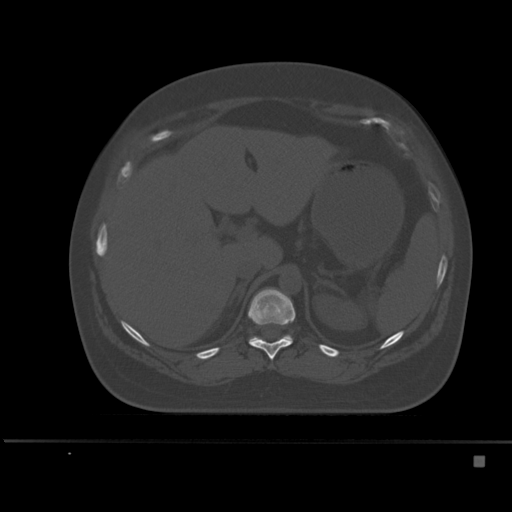
CT including the spine, one axial slice; position 227 of 495 along the scan axis; bone window (W 1800 / L 400 HU); 512 × 512 image matrix, field of view 404 × 404 mm. Patient: female, 33 years. Case-level facts recorded for this patient, not image findings: primary cancer: breast; vertebrae with lytic lesions (as recorded): T1.
Annotated regions visible in this slice (semi-automatically segmented with operator editing):
- T11 vertebra: bounding box (x1, y1, x2, y2) in pixels: (248, 288, 296, 360)
- T12 vertebra: (249, 335, 291, 342)